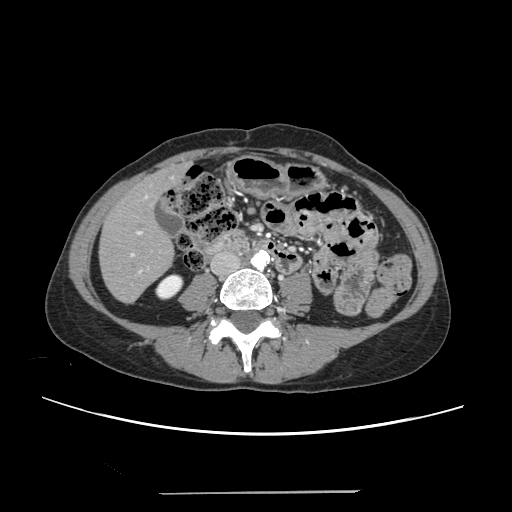
Contrast-enhanced abdominal CT, one axial slice. Slice 62 of 240 in the series (ordered by position). 120 kVp. Intravenous contrast given. Soft-tissue window (W 400 / L 40 HU). 1.25 mm slice thickness. 512 × 512 image matrix, field of view 371 × 371 mm. Female patient, age 60 years. From the clinical record (not read from this slice): diagnosis: colorectal cancer liver metastases, imaged before liver resection; multiple liver metastases: no; largest metastasis: 1.5 cm; disease in both lobes: no.
Outlined on this slice (outlined manually by an expert reader):
- liver: bounding box [x1, y1, x2, y2] px = [101, 168, 183, 302]
- planned liver remnant (the part of the liver to remain after resection): [101, 172, 174, 302]
- portal vein (with intrahepatic branches): [130, 195, 149, 273]